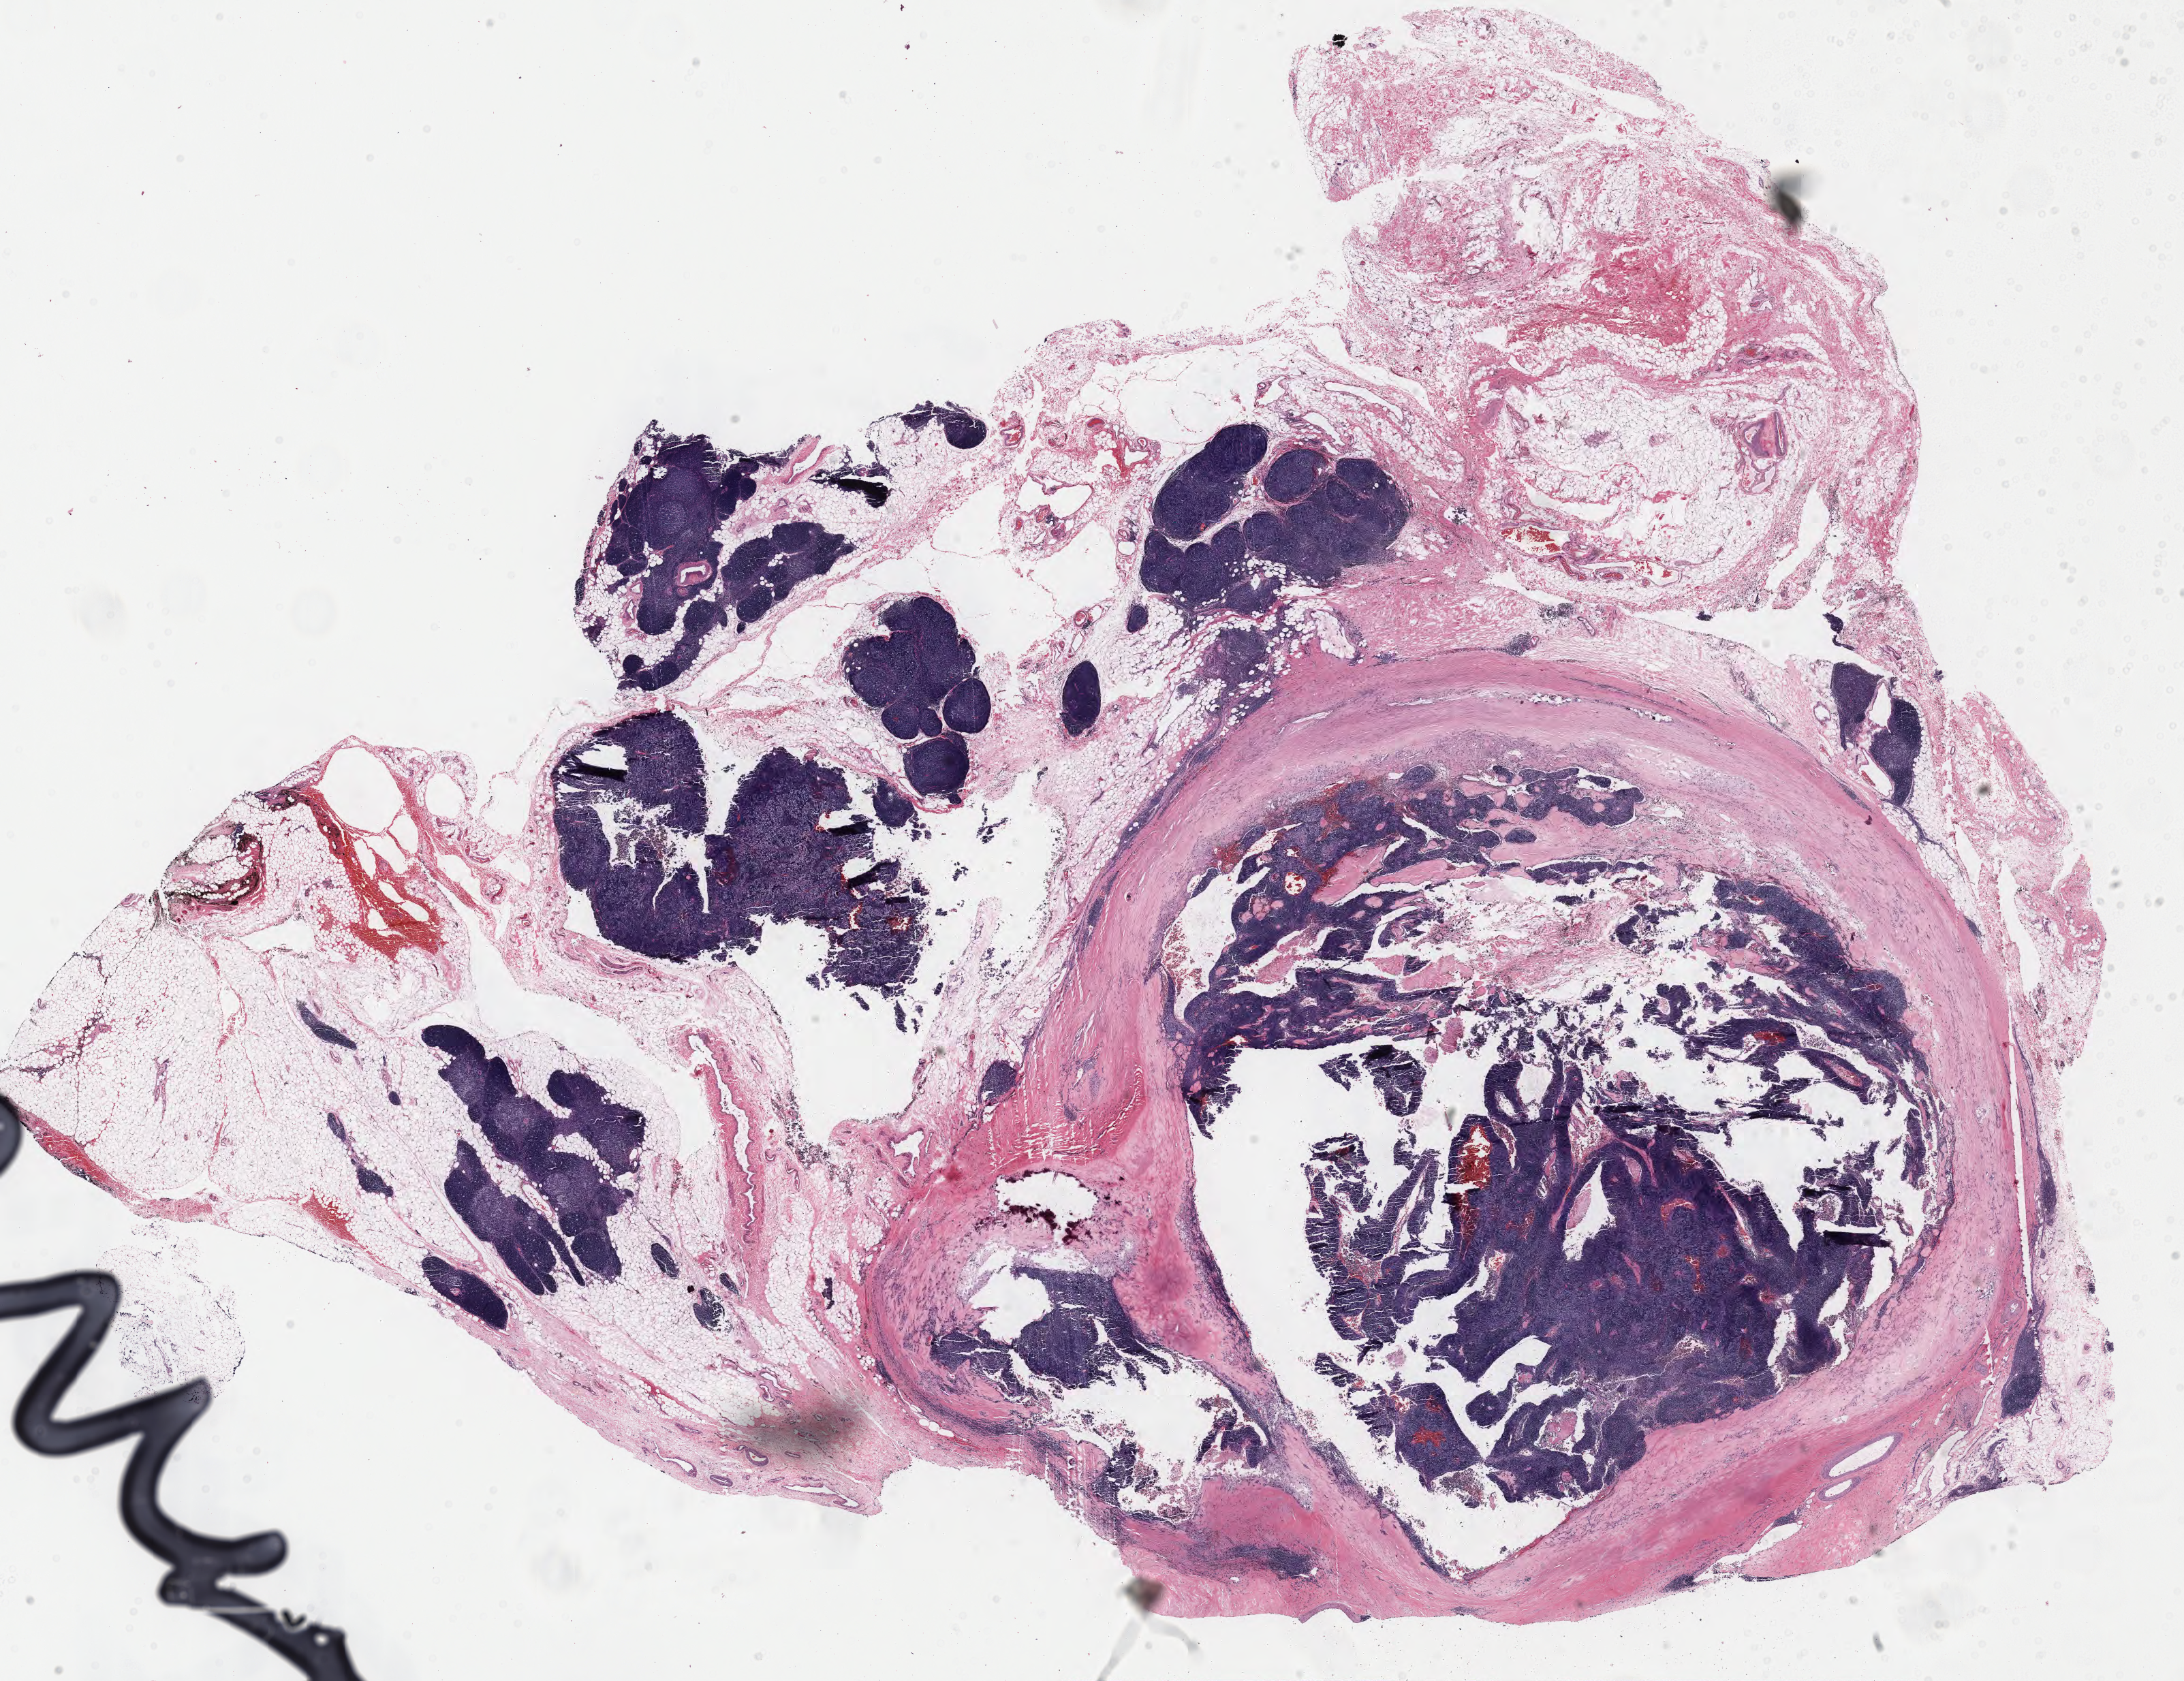
Whole-slide histology image, H&E-stained, a low-resolution overview of the entire scanned area, about 25.4 x 19.6 mm (slide scanned at 40x), formalin-fixed paraffin-embedded (FFPE) diagnostic section, sample: primary tumour, thymus. Patient: male, age at initial diagnosis 44 years.
Histologic diagnosis: Thymoma, type B2, malignant.